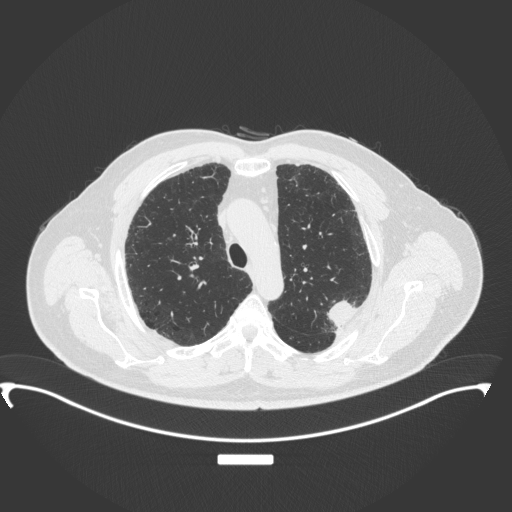
Chest CT, one axial slice; position 267 of 350 along the scan axis; reconstruction kernel B31f; 120 kVp; lung window (W 1500 / L -600 HU); 512 × 512 image matrix. Male patient, age 64 years. From the clinical record (not read from this slice): clinical TNM (as recorded): T1c N1 M1.
Structures marked on this image (bounding box drawn by a radiologist):
- lung tumour (recorded histology: adenocarcinoma): bounding box <323,295,358,335> (left, top, right, bottom; pixels)